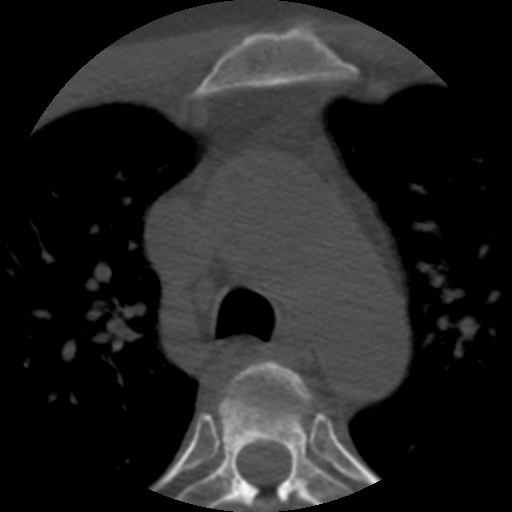
CT including the spine, one axial slice. Position 400 of 508 along the scan axis. Reconstruction kernel STANDARD. Bone window (W 1800 / L 400 HU). 512 × 512 image matrix, field of view 160 × 160 mm. Patient age 57 years. From the clinical record (not read from this slice): primary cancer: prostate.
Structures marked on this image (semi-automatically segmented with operator editing):
- T3 vertebra: bounding box [x1, y1, x2, y2] px = [218, 360, 311, 512]
- T4 vertebra: [178, 388, 352, 512]